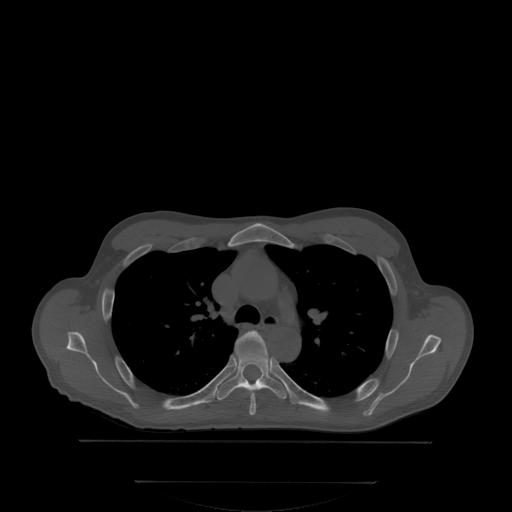
CT including the spine, one axial slice; position 251 of 350 along the scan axis; bone window (W 1800 / L 400 HU); 2.5 mm slice thickness; 512 × 512 image matrix, field of view 500 × 500 mm. Patient: male, 58 years. From the clinical record (not read from this slice): primary cancer: prostate; vertebrae with lytic lesions (as recorded): L1.
Annotated regions visible in this slice (semi-automatically segmented with operator editing):
- T4 vertebra: box from (x=236, y=329) to (x=264, y=414) px
- T5 vertebra: (x=216, y=333)–(x=287, y=400)